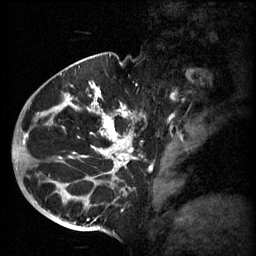
Breast MRI (dynamic contrast-enhanced), one sagittal slice. 3 images stored at this slice position (order not interpretable as contrast timing). 1.5 T. TE 4.2 ms, TR 11 ms. 256 × 256 image matrix. Patient: female, 51 years.
Annotated regions visible in this slice (semi-automatically segmented with operator editing):
- analysis volume of interest (the breast-tissue region the enhancement analysis was run in; not a lesion): bounding box (x1, y1, x2, y2) in pixels: (48, 82, 161, 197)
- tumour enhancement mask (voxels above the 70 % enhancement threshold inside the analysis volume of interest): (50, 84, 139, 185)